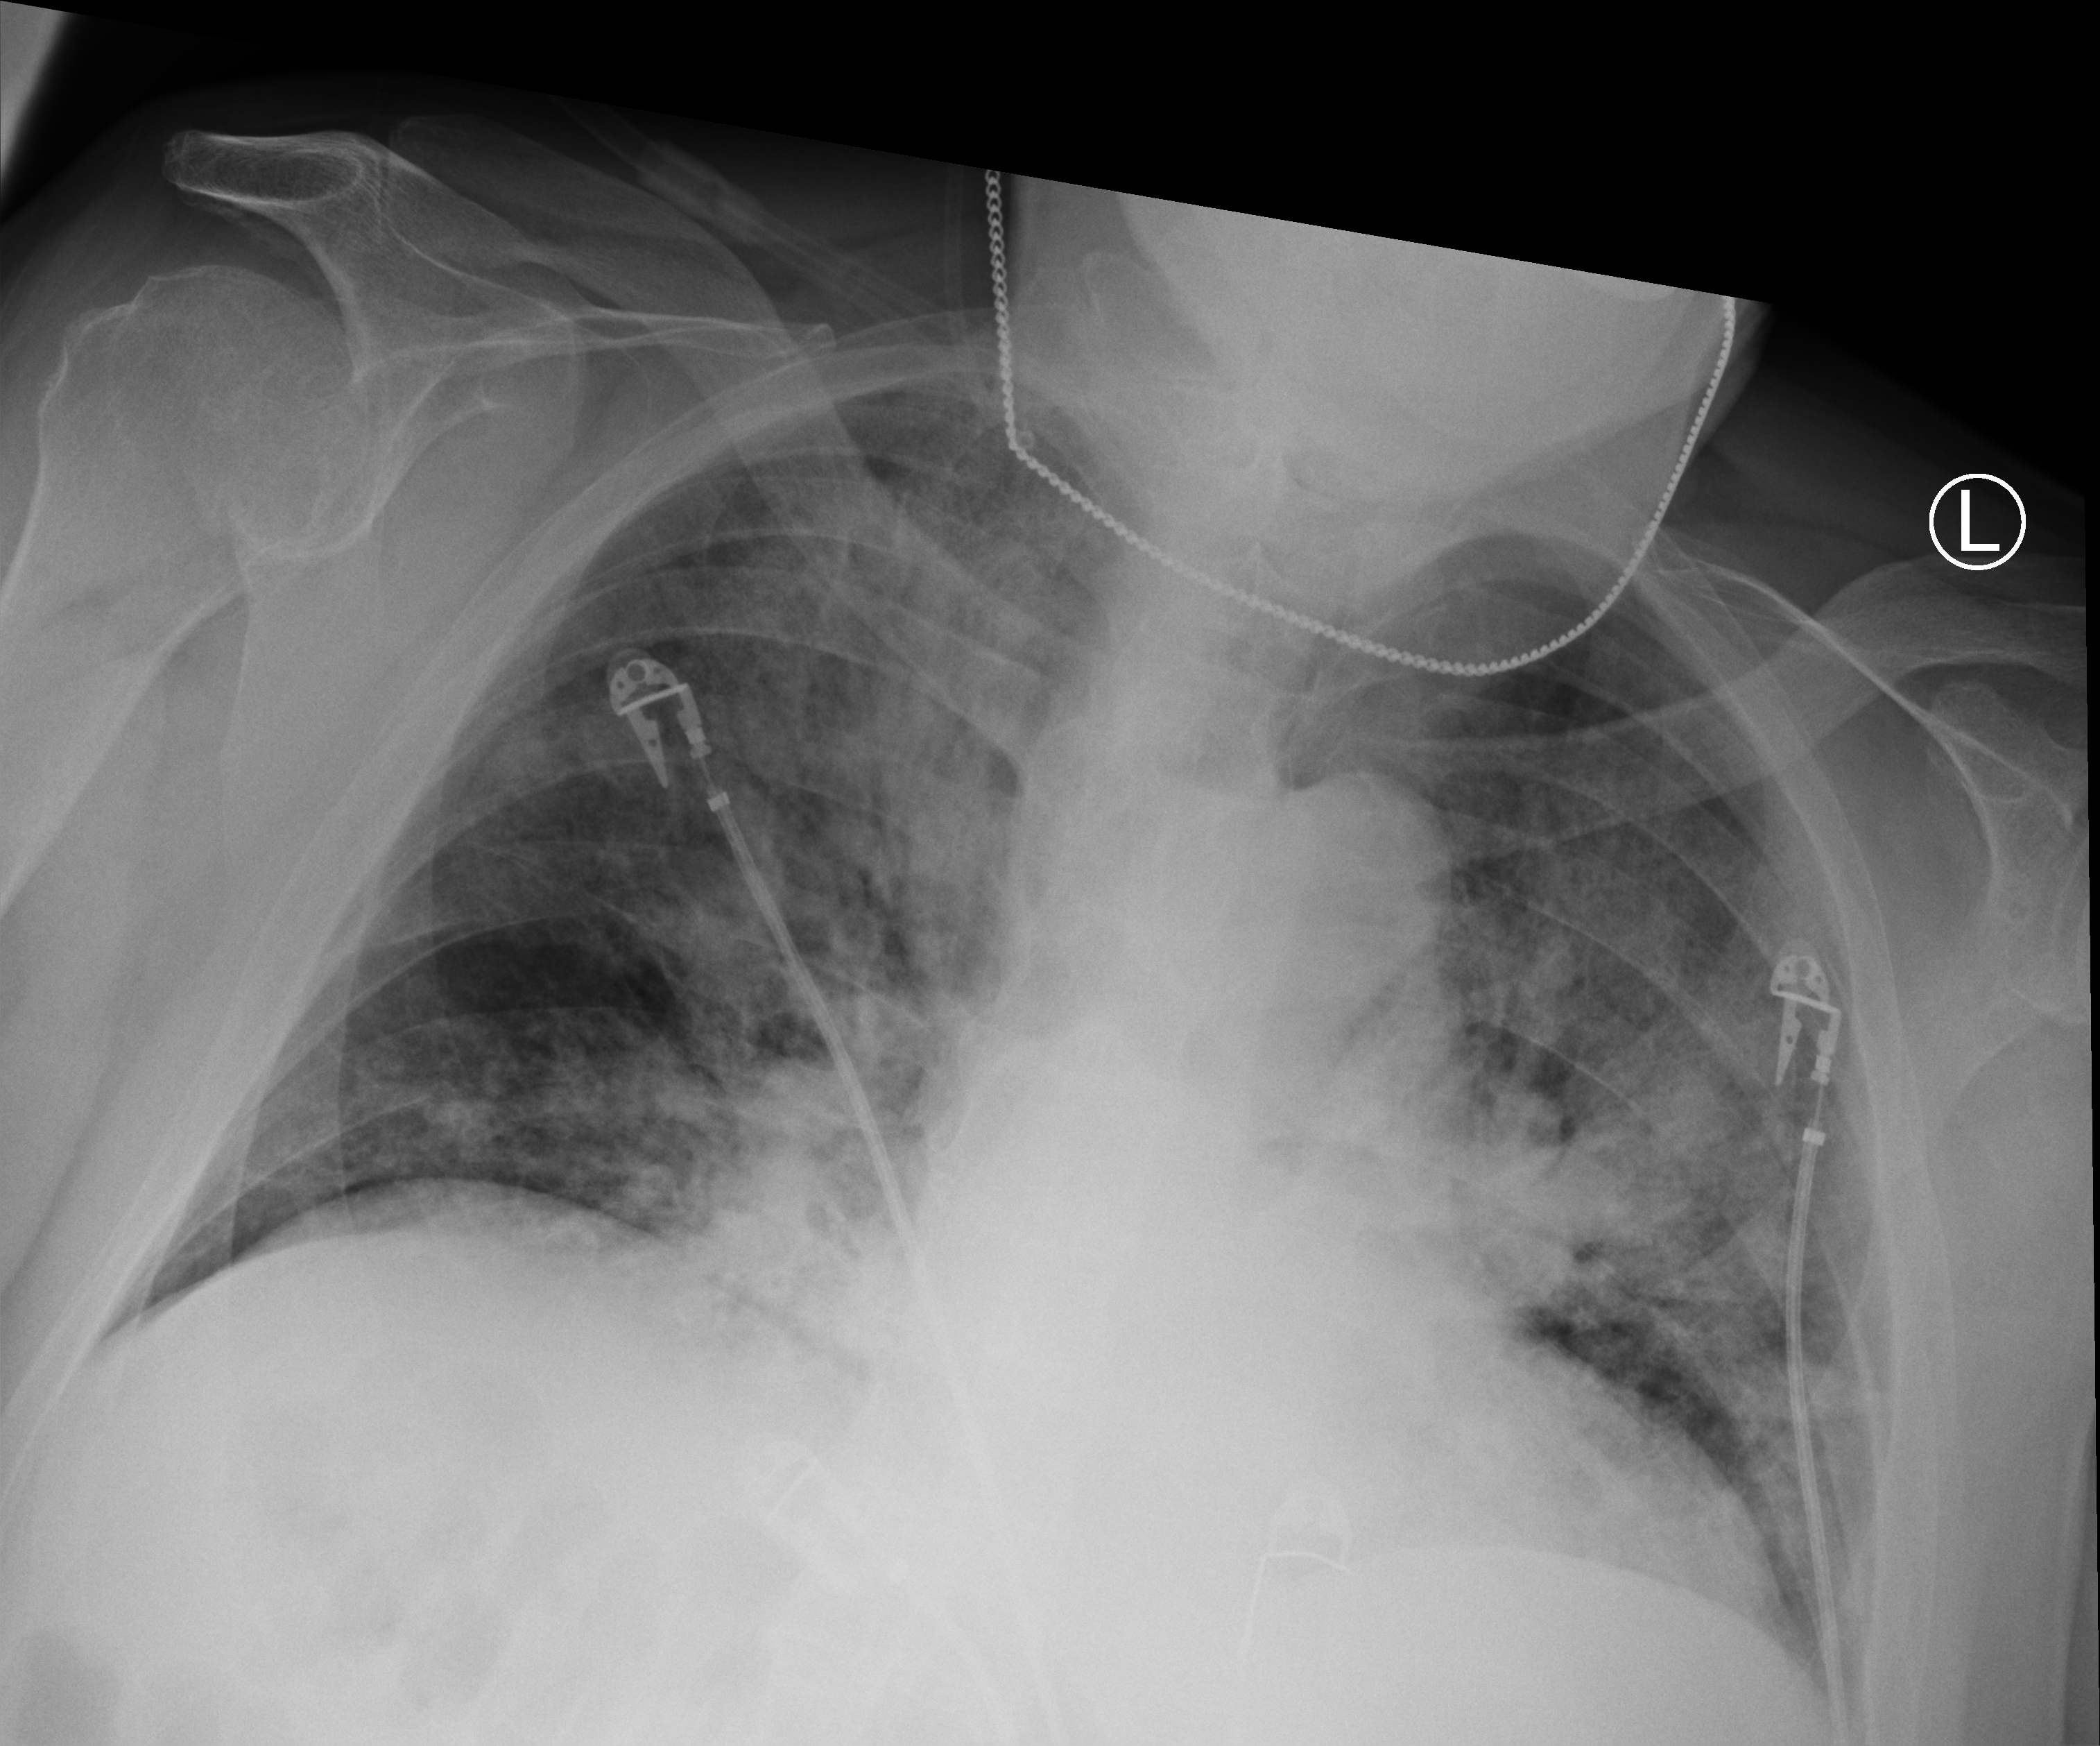
Bedside chest radiograph (computed radiography), anteroposterior (AP) projection. Patient hospitalised with COVID-19; male, aged 75–90 years.
Admission-level facts for this patient (not findings on this image; timing relative to this image not recorded): hypertension (admission record): no; mechanically ventilated during this hospital stay: yes; admitted to intensive care during this hospital stay: yes.